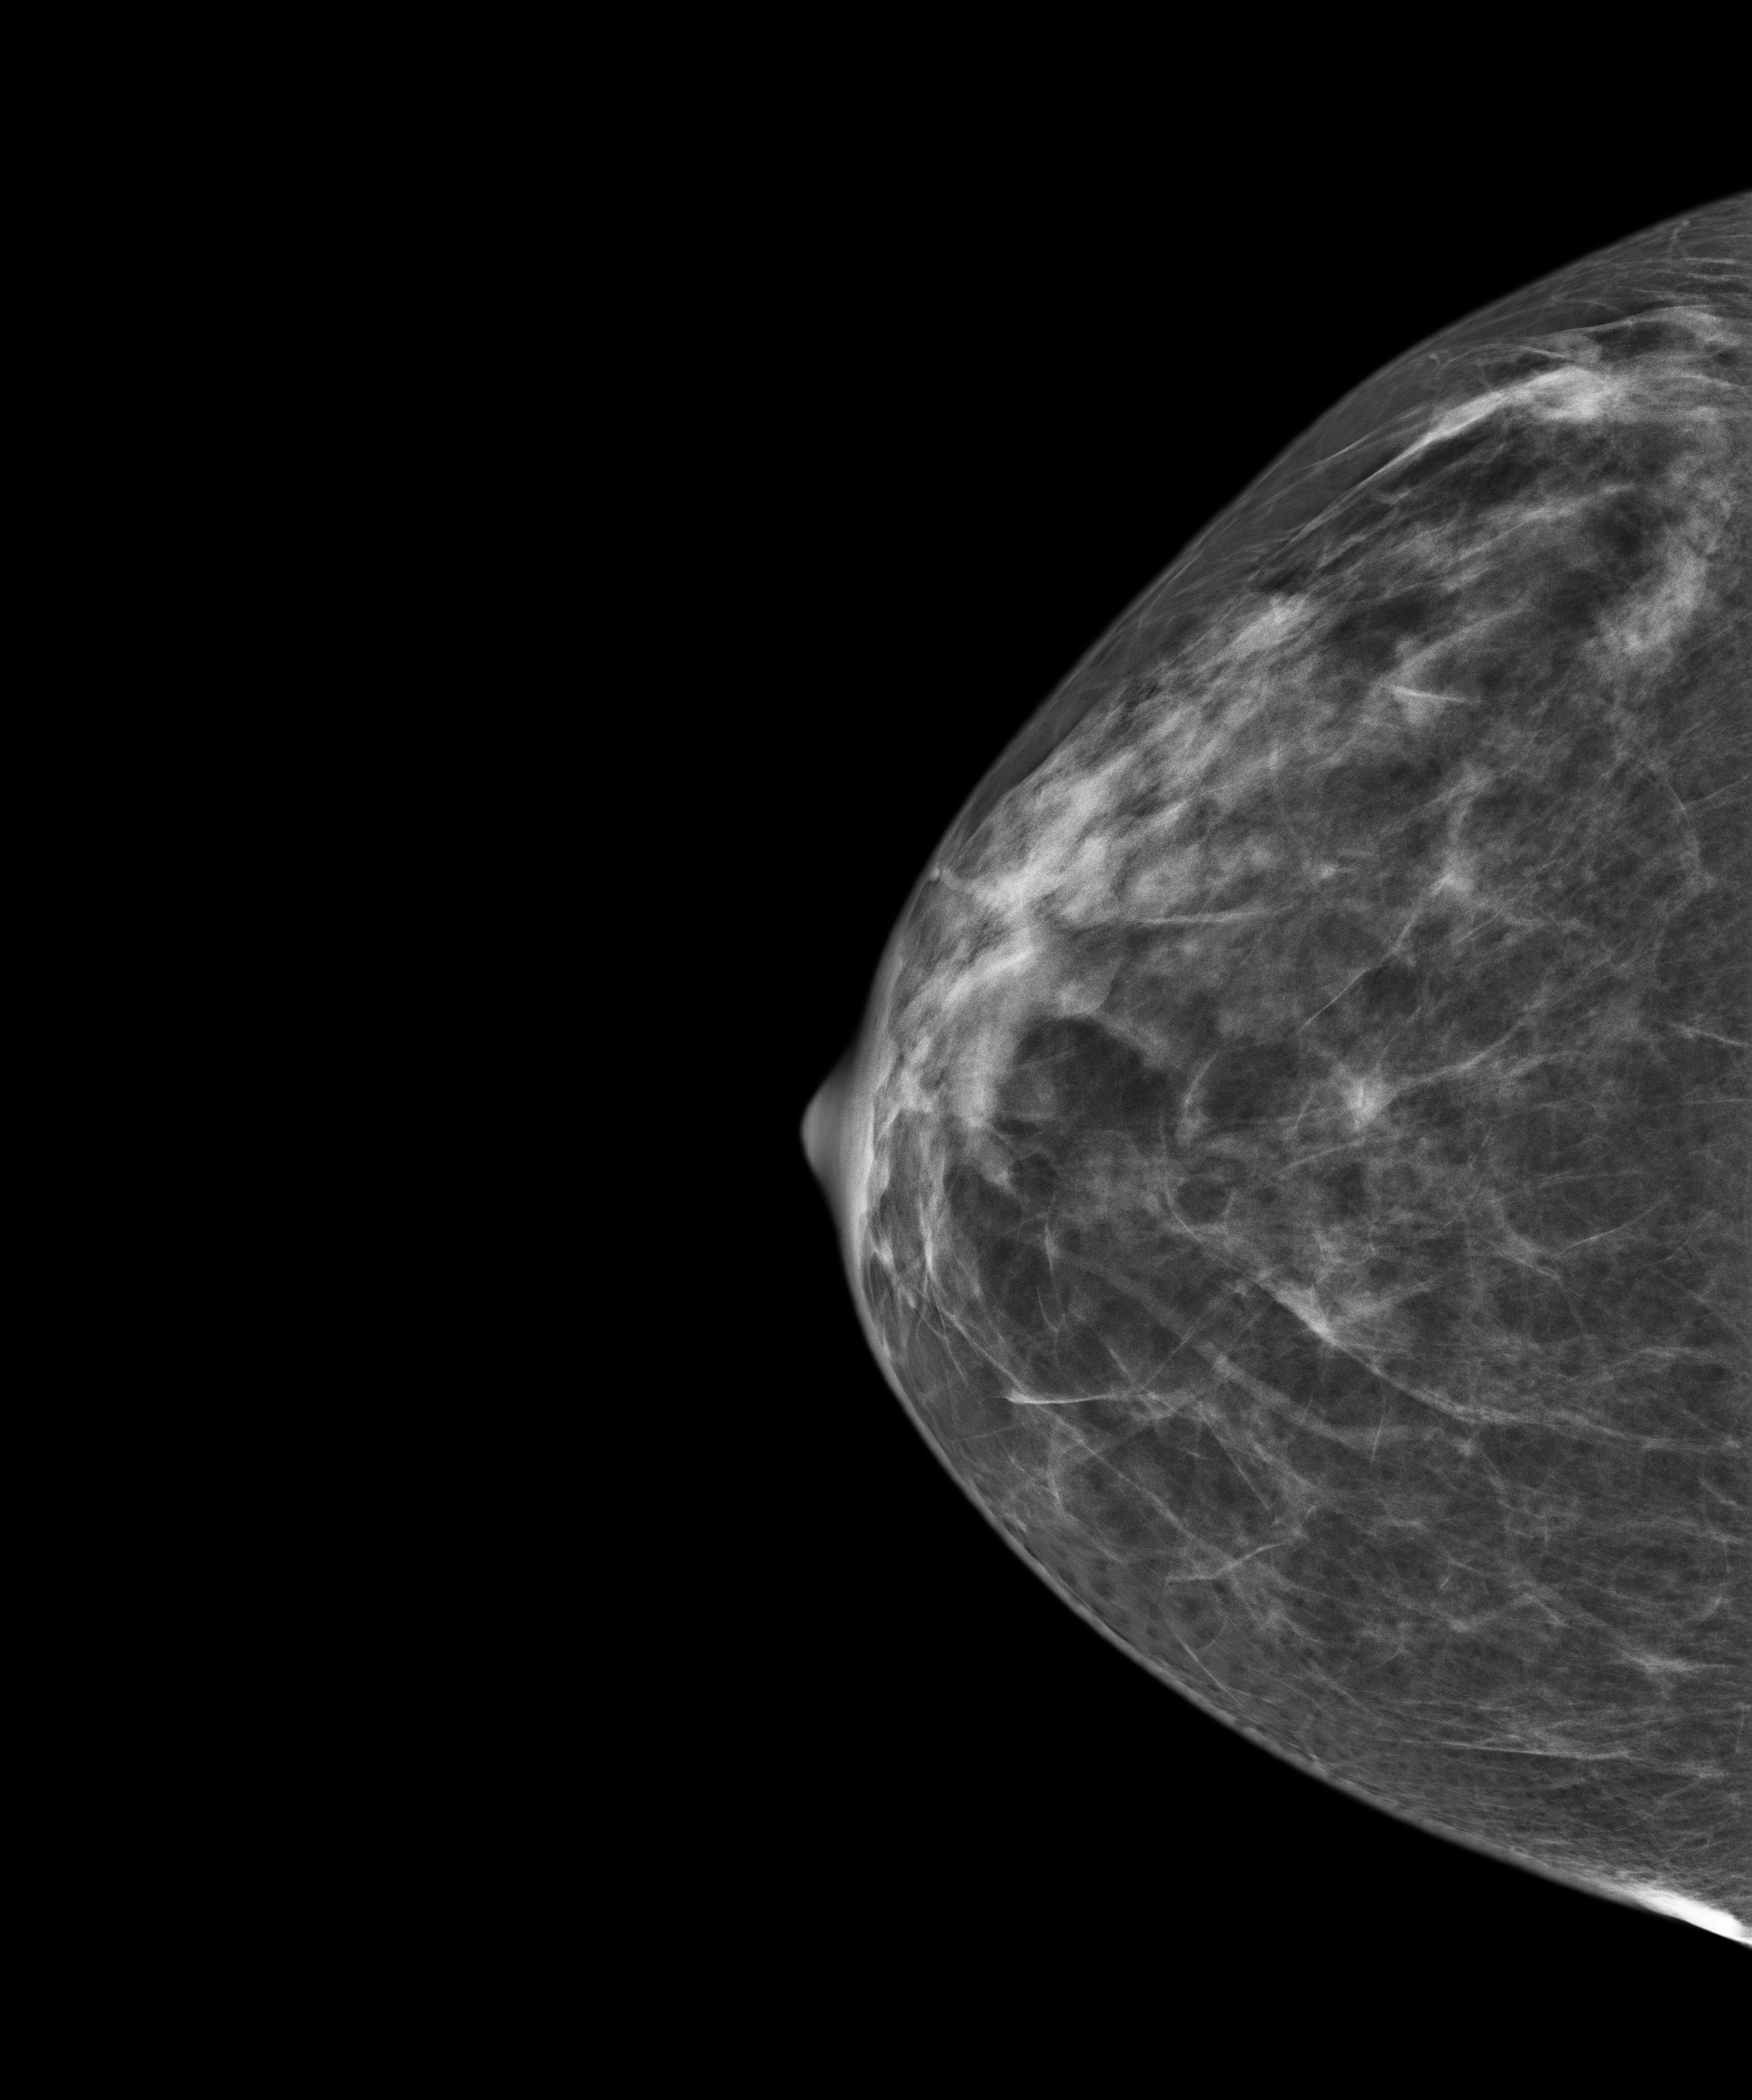
Annual screening mammography examination. Patient aged 43 years (female).
Image type: full-field digital mammogram. Breast: right. Projection: CC view. BI-RADS breast density category at the screening exam (both breasts, scale 1–4): 3. Final BI-RADS category for the screening round (tomosynthesis exam, both breasts): category 1. Recall: no recall after this screen.